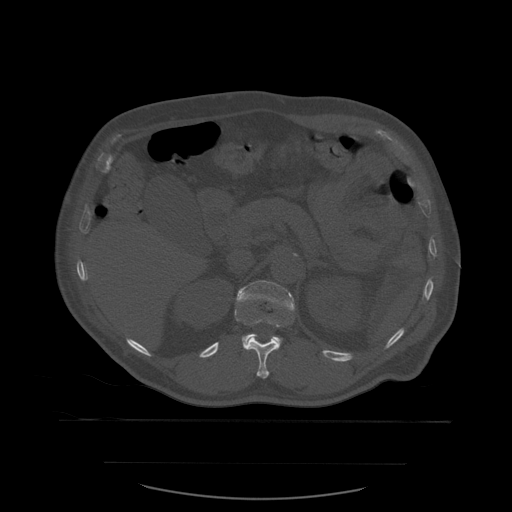
CT including the spine, one axial slice; position 262 of 590 along the scan axis; bone window (W 1800 / L 400 HU); 1.25 mm slice thickness; 512 × 512 image matrix, field of view 479 × 479 mm. Patient age 71 years. From the clinical record (not read from this slice): primary cancer: lung.
Structures marked on this image (semi-automatic segmentation, software-assisted and operator-edited):
- L1 vertebra: box from (x=235, y=281) to (x=295, y=343) px
- T12 vertebra: (x=235, y=310)–(x=281, y=379)